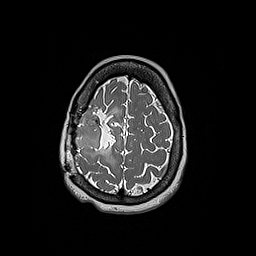
Brain MRI from a brain-tumour surgery series, one axial slice; position 51 of 192 along the scan axis; 1 mm slice thickness; 256 × 256 image matrix. From the clinical record (not read from this slice): histopathology: Oligodendroglioma; WHO grade: 3; IDH mutation: yes; tumour location: Right Frontal.
Outlined on this slice (expert manual segmentation):
- tumour: bounding box [x1, y1, x2, y2] px = [75, 112, 103, 153]